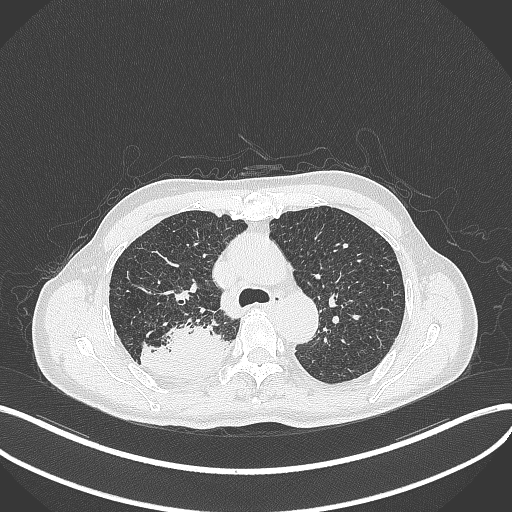
Chest CT, one axial slice; position 317 of 428 along the scan axis; reconstruction kernel B70f; 120 kVp; lung window (W 1500 / L -600 HU); 1 mm slice thickness; 512 × 512 image matrix, field of view 400 × 400 mm. Patient: male, 79 years. Case-level facts recorded for this patient, not image findings: clinical TNM (as recorded): T3 N0 M0.
Structures marked on this image (rectangle marked by the reading radiologist):
- lung tumour (recorded histology: adenocarcinoma): bounding box (x1, y1, x2, y2) in pixels: (138, 314, 230, 375)